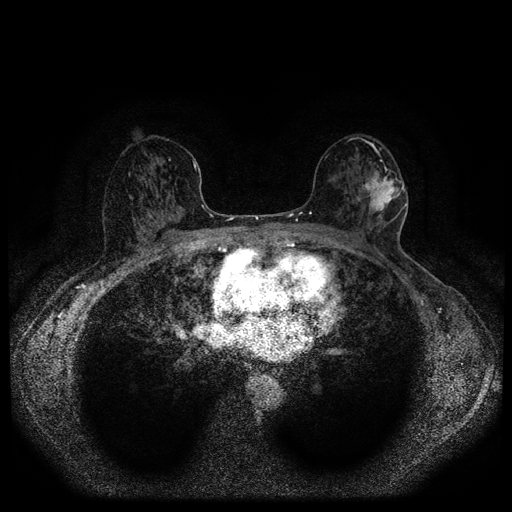
Breast MRI (dynamic contrast-enhanced, multi-phase), one axial slice; position 58 of 116 along the scan axis; dynamic contrast-enhanced series, time point 2 of 5 at this slice position (early post-contrast); 1.5 T; TE 2.7 ms, TR 5.4 ms; 512 × 512 image matrix, field of view 330 × 330 mm. Patient: female, 56 years.
Annotated regions visible in this slice (semi-automatically segmented with operator editing):
- breast lesion (labelled 'tumour' in the annotation; benign lesions carry a separate 'benign' label): bounding box <359,164,403,214> (left, top, right, bottom; pixels)